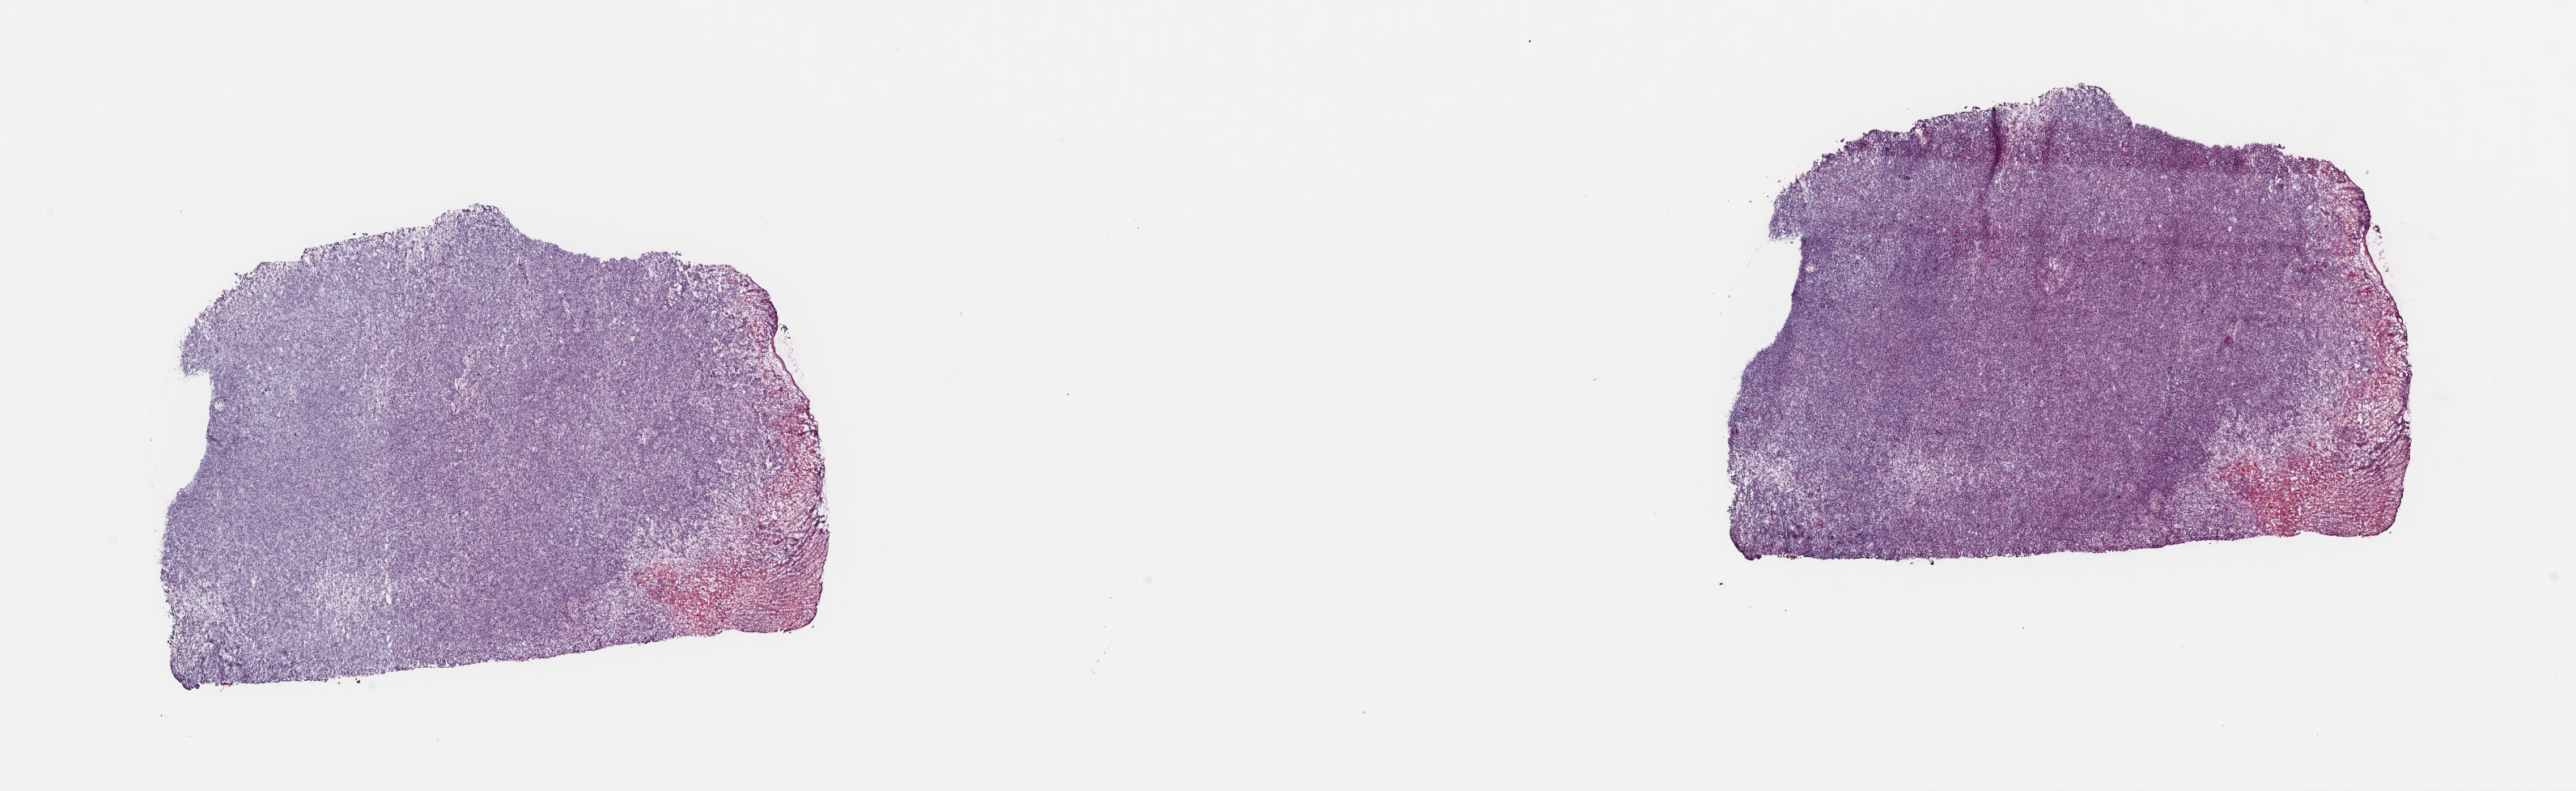
H&E-stained whole-slide image — low-resolution overview of the scanned area, about 25.1 x 7.7 mm; frozen section from the top of the tissue portion; head and neck, primary tumour sample. Male, age 62 years at initial diagnosis. Histologic grade: G3 (poorly differentiated). Composition of this section per pathologist review: tumour cells 97%, tumour nuclei 75%, normal cells 0%, stromal cells 0%, necrosis 3%. Infiltration values recorded for this section: lymphocyte infiltration 7%, monocyte infiltration 0%, neutrophil infiltration 0%.
- diagnosis: Squamous cell carcinoma, large cell, nonkeratinizing, NOS
- laterality: midline
- AJCC pathologic stage: III (7th edition)